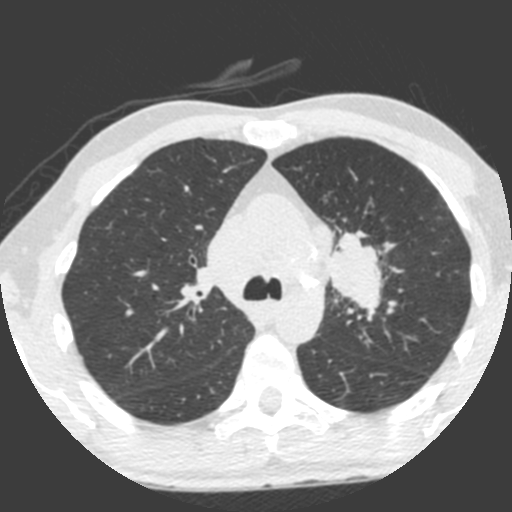
Low-dose screening chest CT, axial slice; third annual screen; lung window (W 1500 / L -600 HU); 2 mm slice thickness; 120 kVp. Male, age 55 years at enrolment. Current smoker at enrolment.
• Expert reader's lesion annotation, bounding box <308,230,390,323> (left, top, right, bottom; pixels).
• Screening reader's record for this exam (one nodule recorded; not confirmed to be the boxed lesion): non-calcified nodule or mass ≥4 mm, left upper lobe, 49 × 29 mm, spiculated (stellate) margins, soft tissue attenuation, pre-existing on the prior screen: yes; interval growth: yes.
• Later outcome: lung cancer diagnosed 0 days after this screen — small cell carcinoma, NOS, left upper lobe, undifferentiated (G4), stage IV (AJCC 6th edition), 60 mm at pathology.